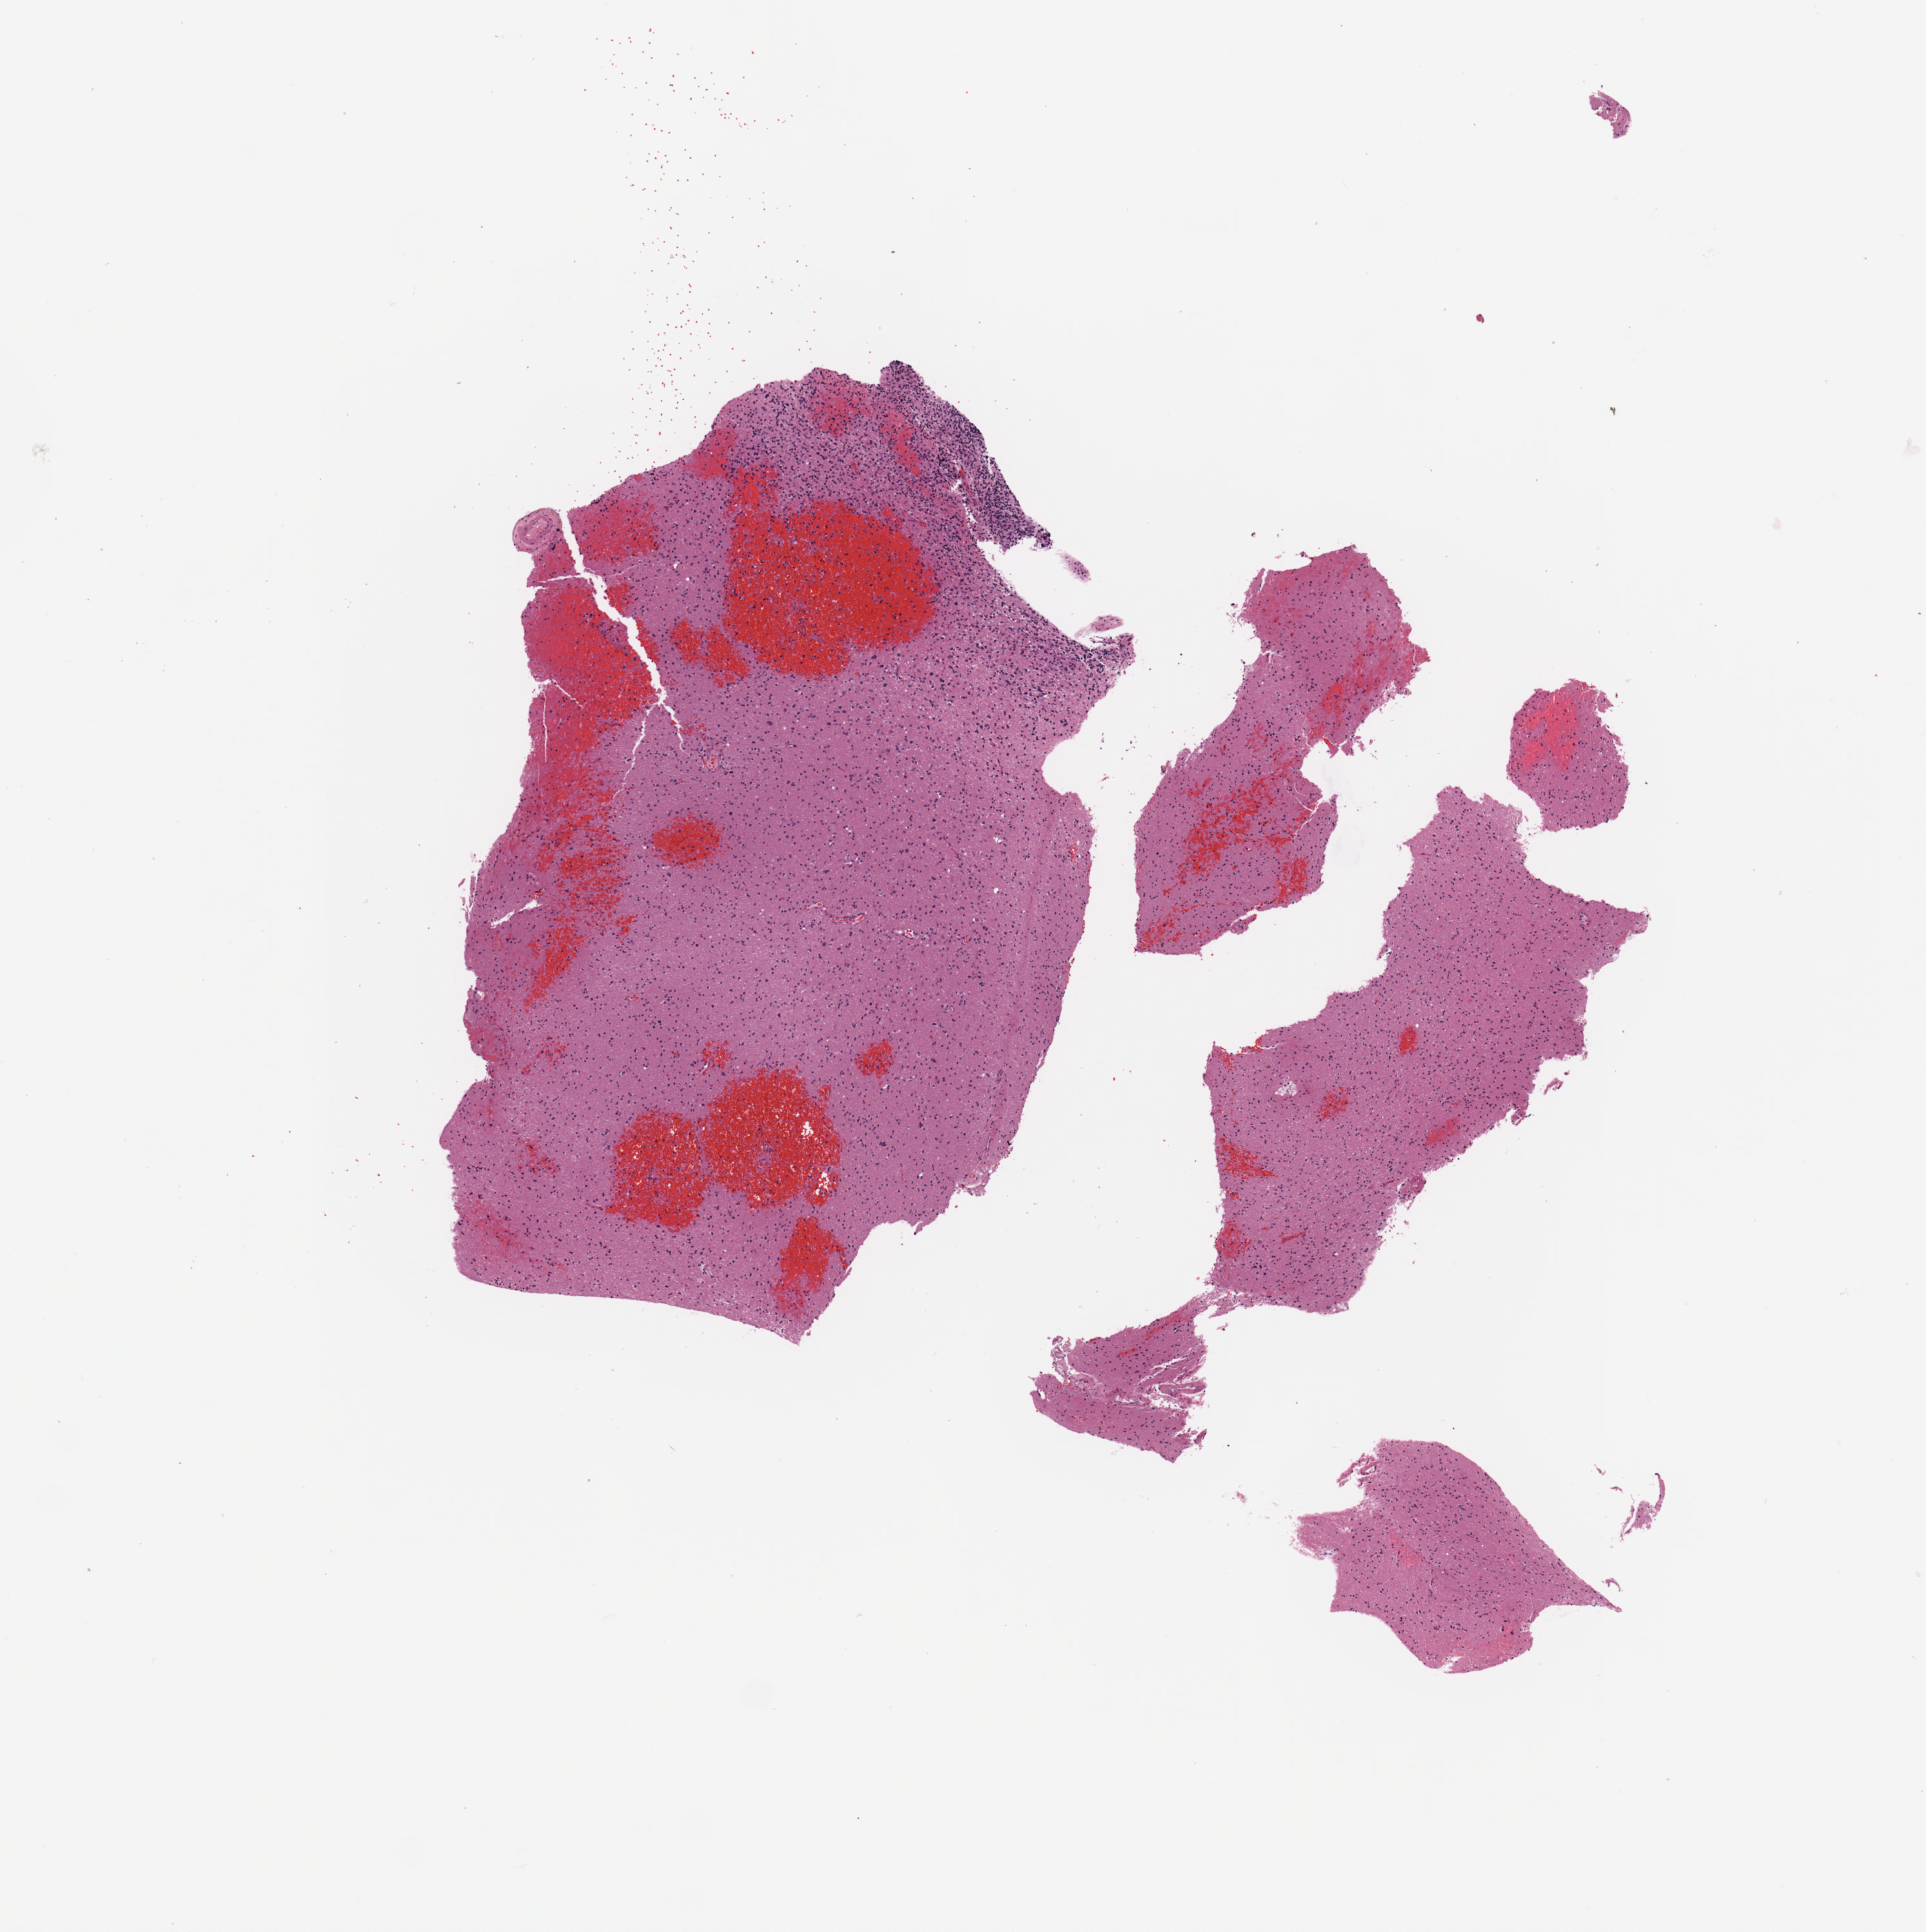
Digitized Hematoxylin and eosin (H&E) stained tissue section (whole slide), whole scanned area (about 5.9 x 5.9 mm, slide scanned at 20x) shown as a low-resolution overview. Tumour tissue sample, sampled site: brain. Female, 75 y/o. Pathologist review of this section (percent, as recorded): tumour nuclei 60%, necrosis 0%.
Primary tumour site (as recorded): temporal lobe. Diagnosis: Glioblastoma.